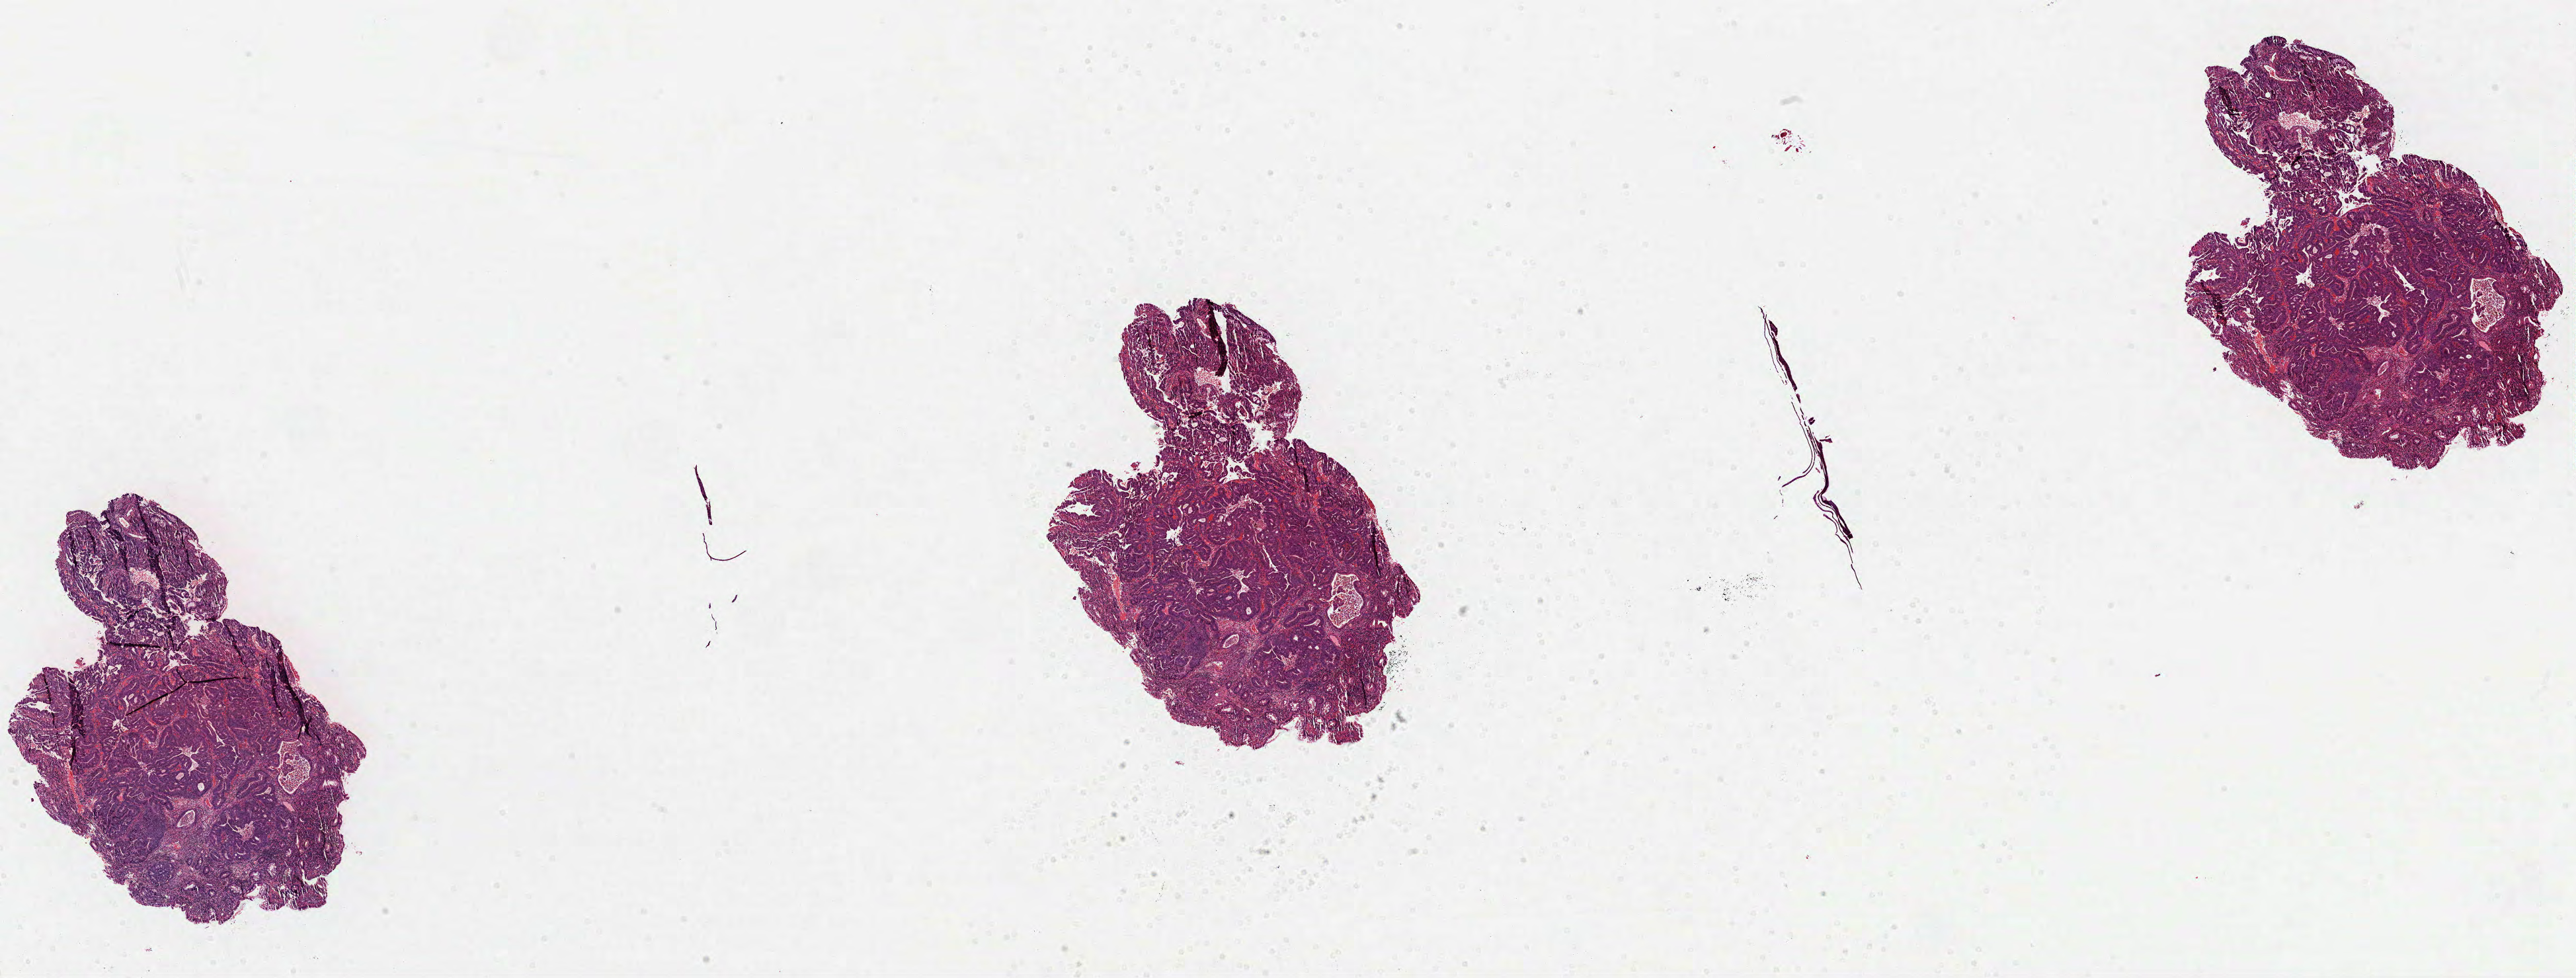
Hematoxylin and eosin (H&E) stained whole-slide image — shown as a low-resolution overview of the whole scanned area (about 31.4 x 11.9 mm, acquisition: 40x scan), formalin-fixed paraffin-embedded (FFPE) diagnostic section, primary tumour sample from the rectum. Male, age 75 years at initial diagnosis.
Diagnosis: Adenocarcinoma, NOS.